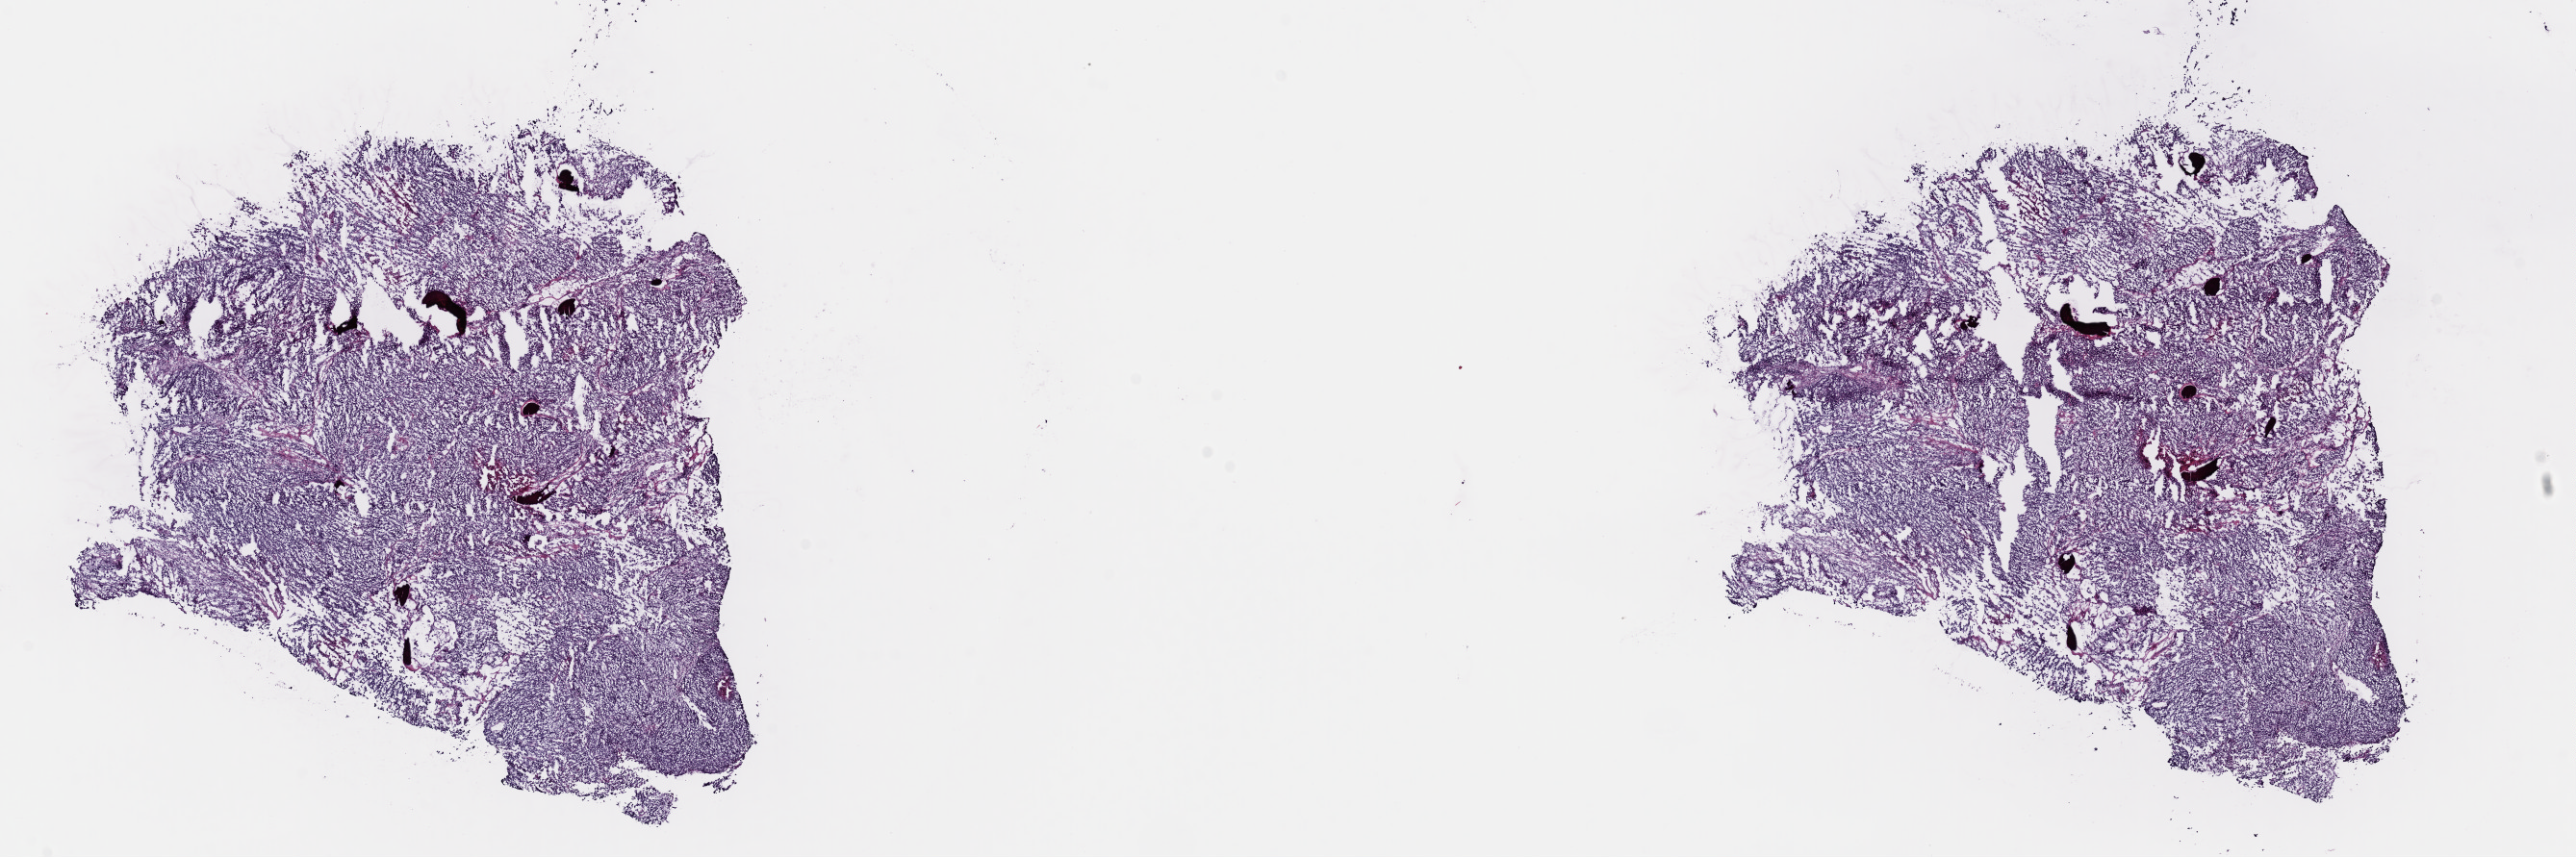
H&E whole-slide image — low-resolution overview of the scanned area, about 21.1 x 7.0 mm (acquisition: 40x scan); frozen section from the top of the tissue portion; metastatic tumour sample, sampled site not recorded. Female patient; age at initial diagnosis 32 years. Slide review estimates, as recorded: tumour cells 100%, tumour nuclei 95%, normal cells 0%, stromal cells 0%, necrosis 0%. Inflammatory infiltration, as recorded: lymphocyte infiltration 0%, monocyte infiltration 0%, neutrophil infiltration 0%.
This section: metastatic tumour tissue. Patient diagnosis: Malignant melanoma, NOS.